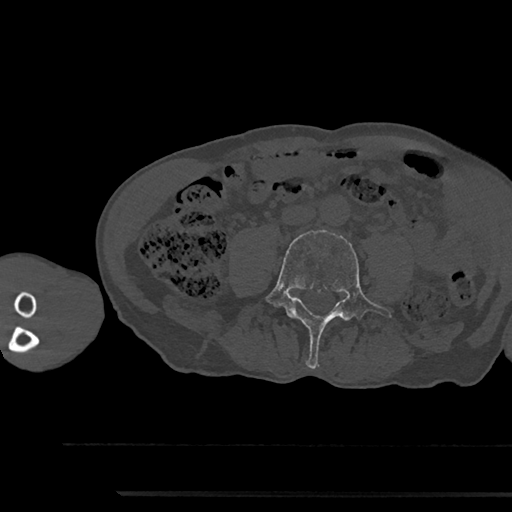
CT including the spine, one axial slice. Slice 416 of 797 in the series (ordered by position). Reconstruction kernel Br40s/3. Bone window (W 1800 / L 400 HU). 0.5 mm slice thickness. 512 × 512 image matrix. Male patient, age 79 years. From the clinical record (not read from this slice): primary cancer: prostate.
Outlined on this slice (semi-automatic segmentation, software-assisted and operator-edited):
- L4 vertebra: bounding box (x1, y1, x2, y2) in pixels: (265, 230, 392, 369)